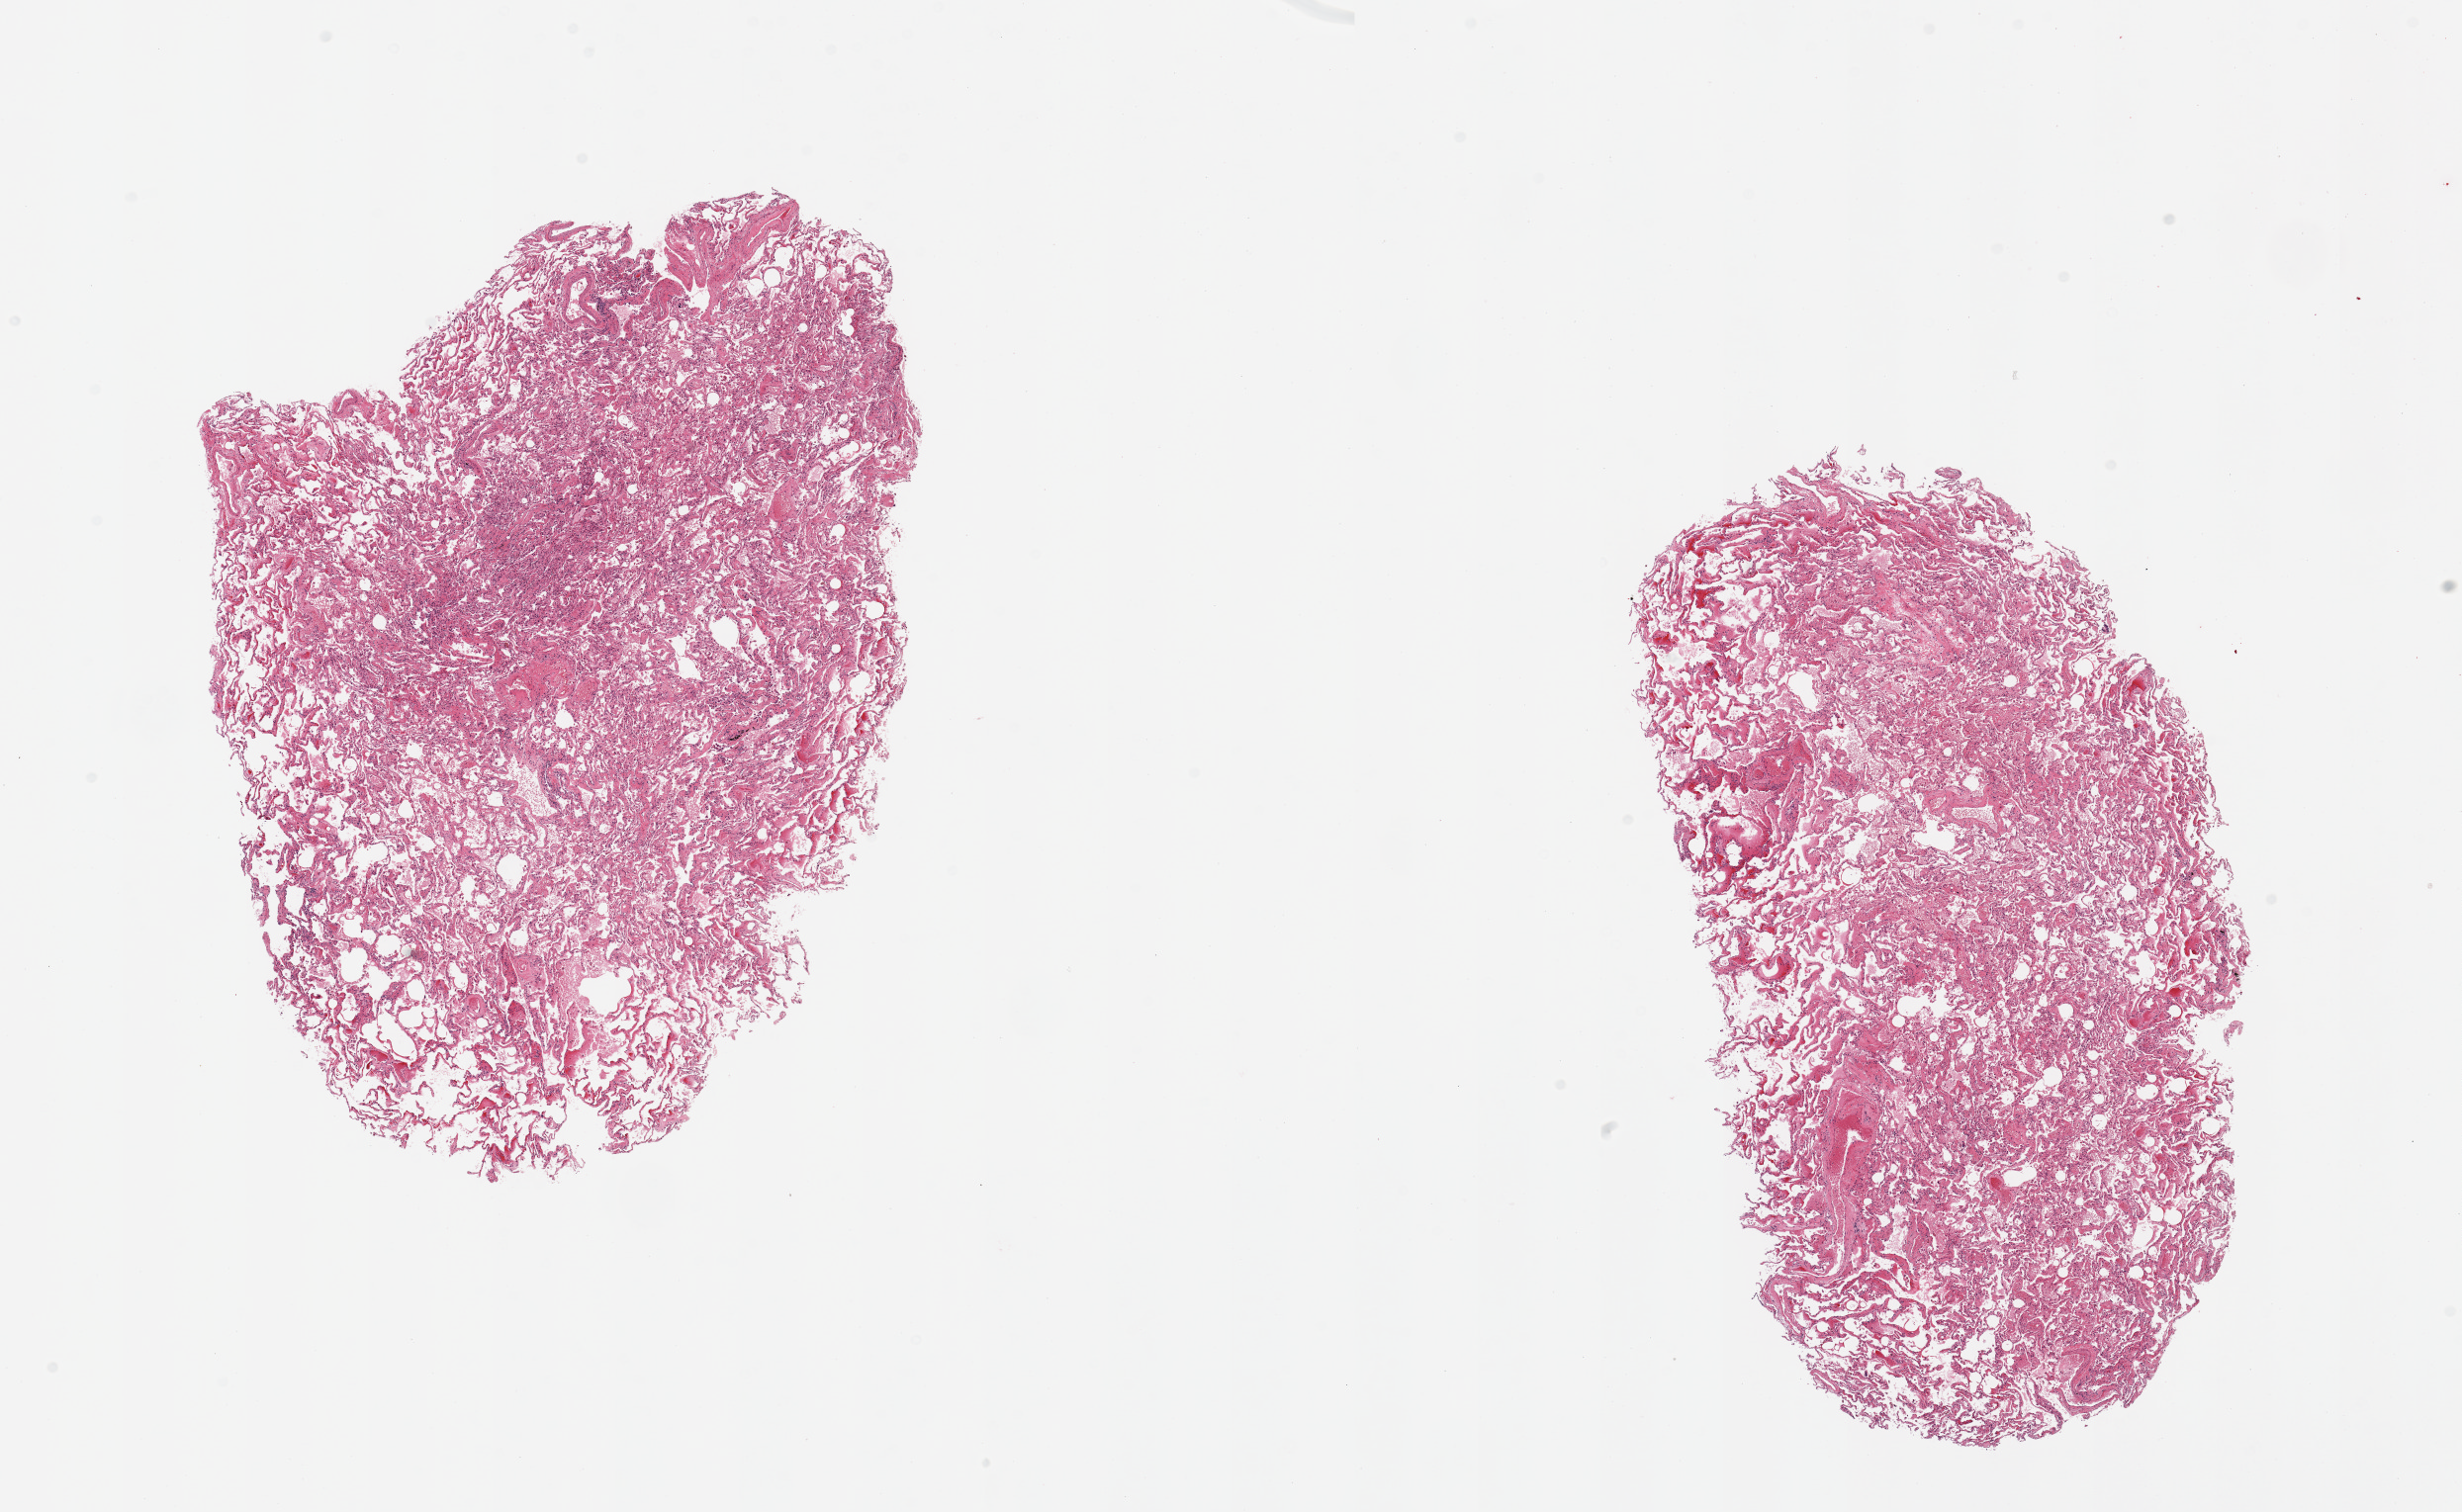
Whole-slide image, H&E stain — whole scanned area (about 19.7 x 12.1 mm, slide scanned at 20x) shown as a low-resolution overview, PAXgene-fixed, paraffin-embedded tissue, sampled site (target tissue): lung, donor tissue sample. Donor: male.
Review note (as recorded): 2 pieces; congestion and focal atelectasis.